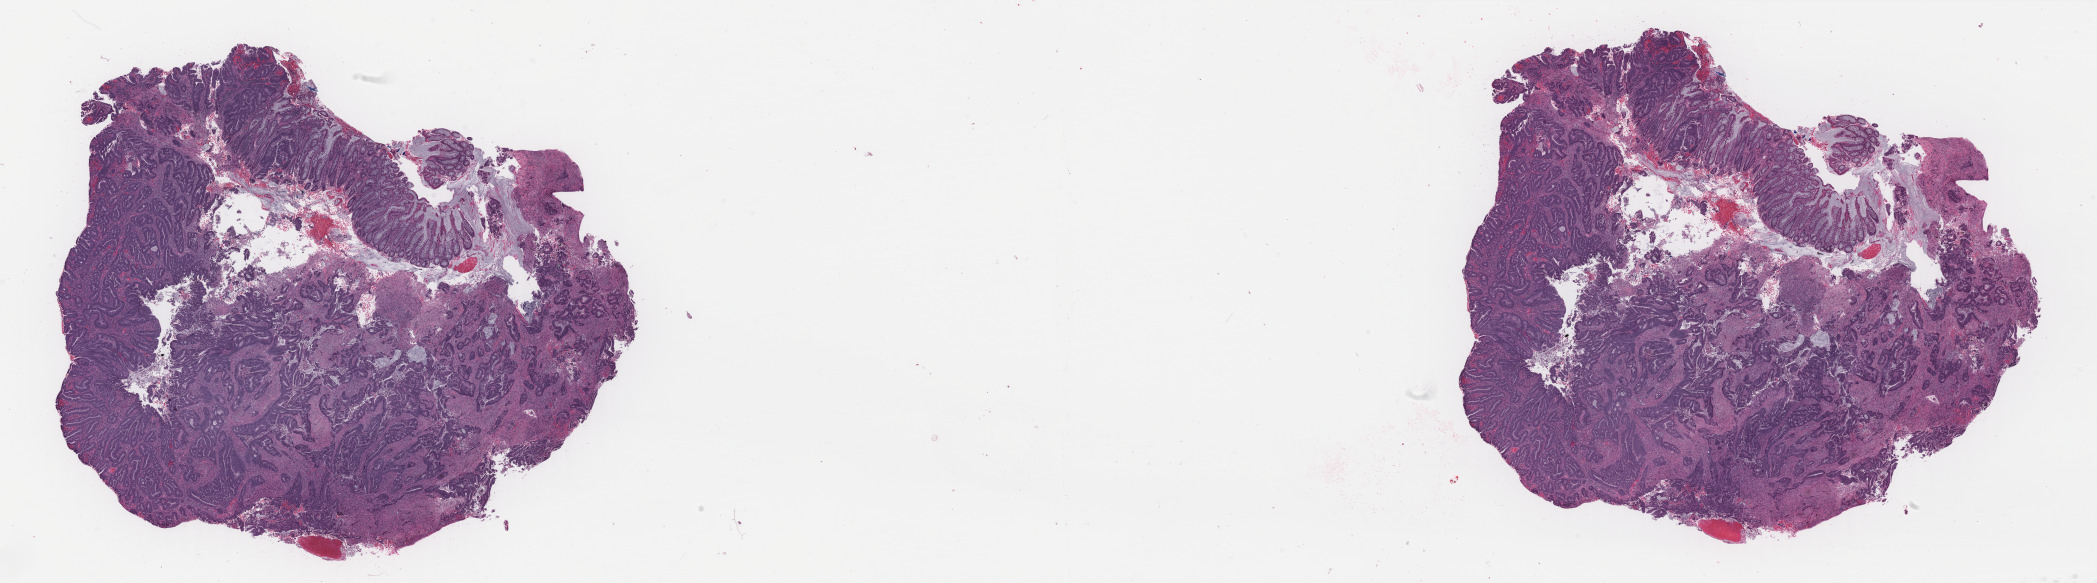
Hematoxylin and eosin (H&E) stained whole-slide image, low-resolution overview of the scanned area, about 33.2 x 9.2 mm (from a 40x scan), FFPE section, colon, primary tumour sample. Female, age 55 years at initial diagnosis.
• AJCC pathologic stage: IIA
• histologic diagnosis: Adenocarcinoma, NOS